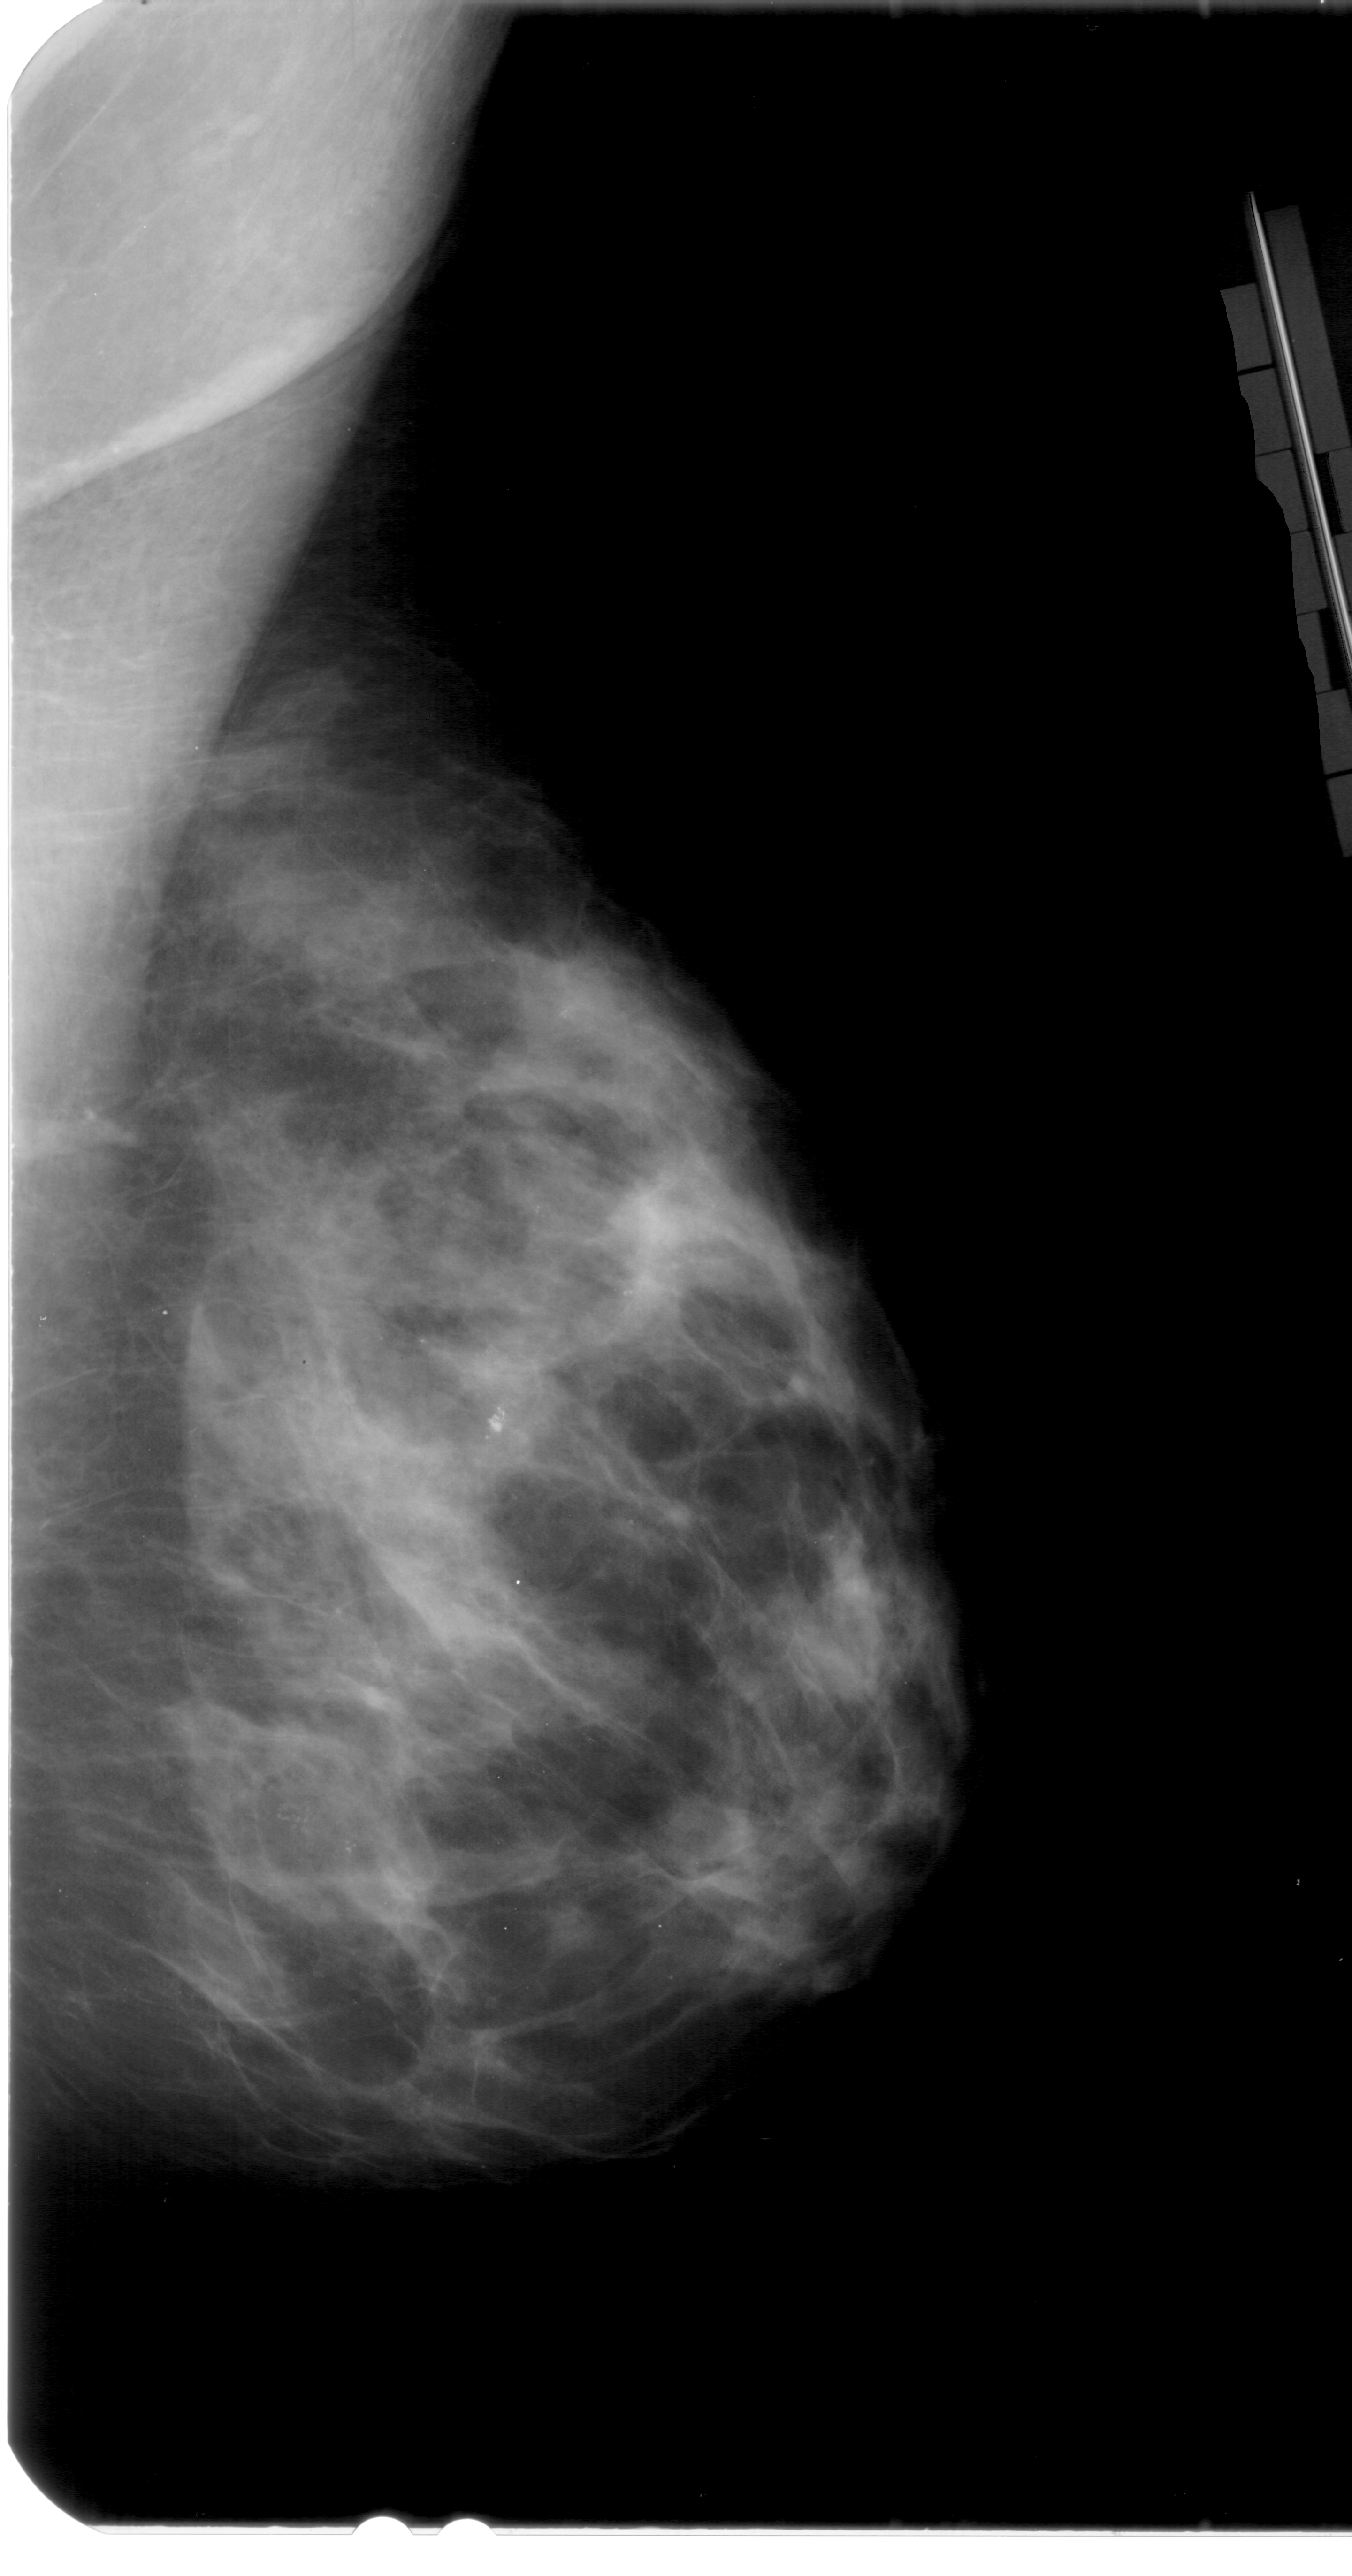
Scanned film-screen mammogram; right breast; mediolateral oblique (MLO) view; BI-RADS breast density category 4 (scale 1–4); 1352 × 2576 image matrix.
Marked abnormalities (boxes around the expert regions of interest):
- calcifications, morphology pleomorphic, distribution clustered; BI-RADS assessment category 4; subtlety rating 3 on a 1 (subtle) to 5 (obvious) scale; pathology (as recorded): benign: bounding box (x1, y1, x2, y2) in pixels: (471, 1382, 547, 1448)